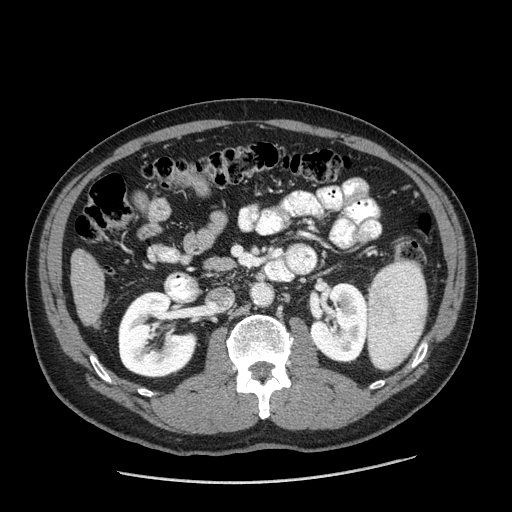
Contrast-enhanced abdominal CT (liver protocol), one axial slice. Slice 55 of 198 in the series (ordered by position). Reconstruction kernel STANDARD. 120 kVp. One of 2 acquisitions stored at this slice position. Soft-tissue window (W 400 / L 40 HU). 512 × 512 image matrix, field of view 400 × 400 mm. Case-level facts recorded for this patient, not image findings: diagnosis: hepatocellular carcinoma (patient treated with transarterial chemoembolisation; whether this scan precedes or follows treatment is not stated here); TNM stage (as recorded): Stage-II; Child-Pugh class: A; tumour differentiation: moderately differentiated.
Structures marked on this image (semi-automatic segmentation, software-assisted and operator-edited):
- liver parenchyma outside the tumour (the mass and vessels are separate outlines, so this box may not span the whole liver): bounding box (x1, y1, x2, y2) in pixels: (70, 250, 104, 324)